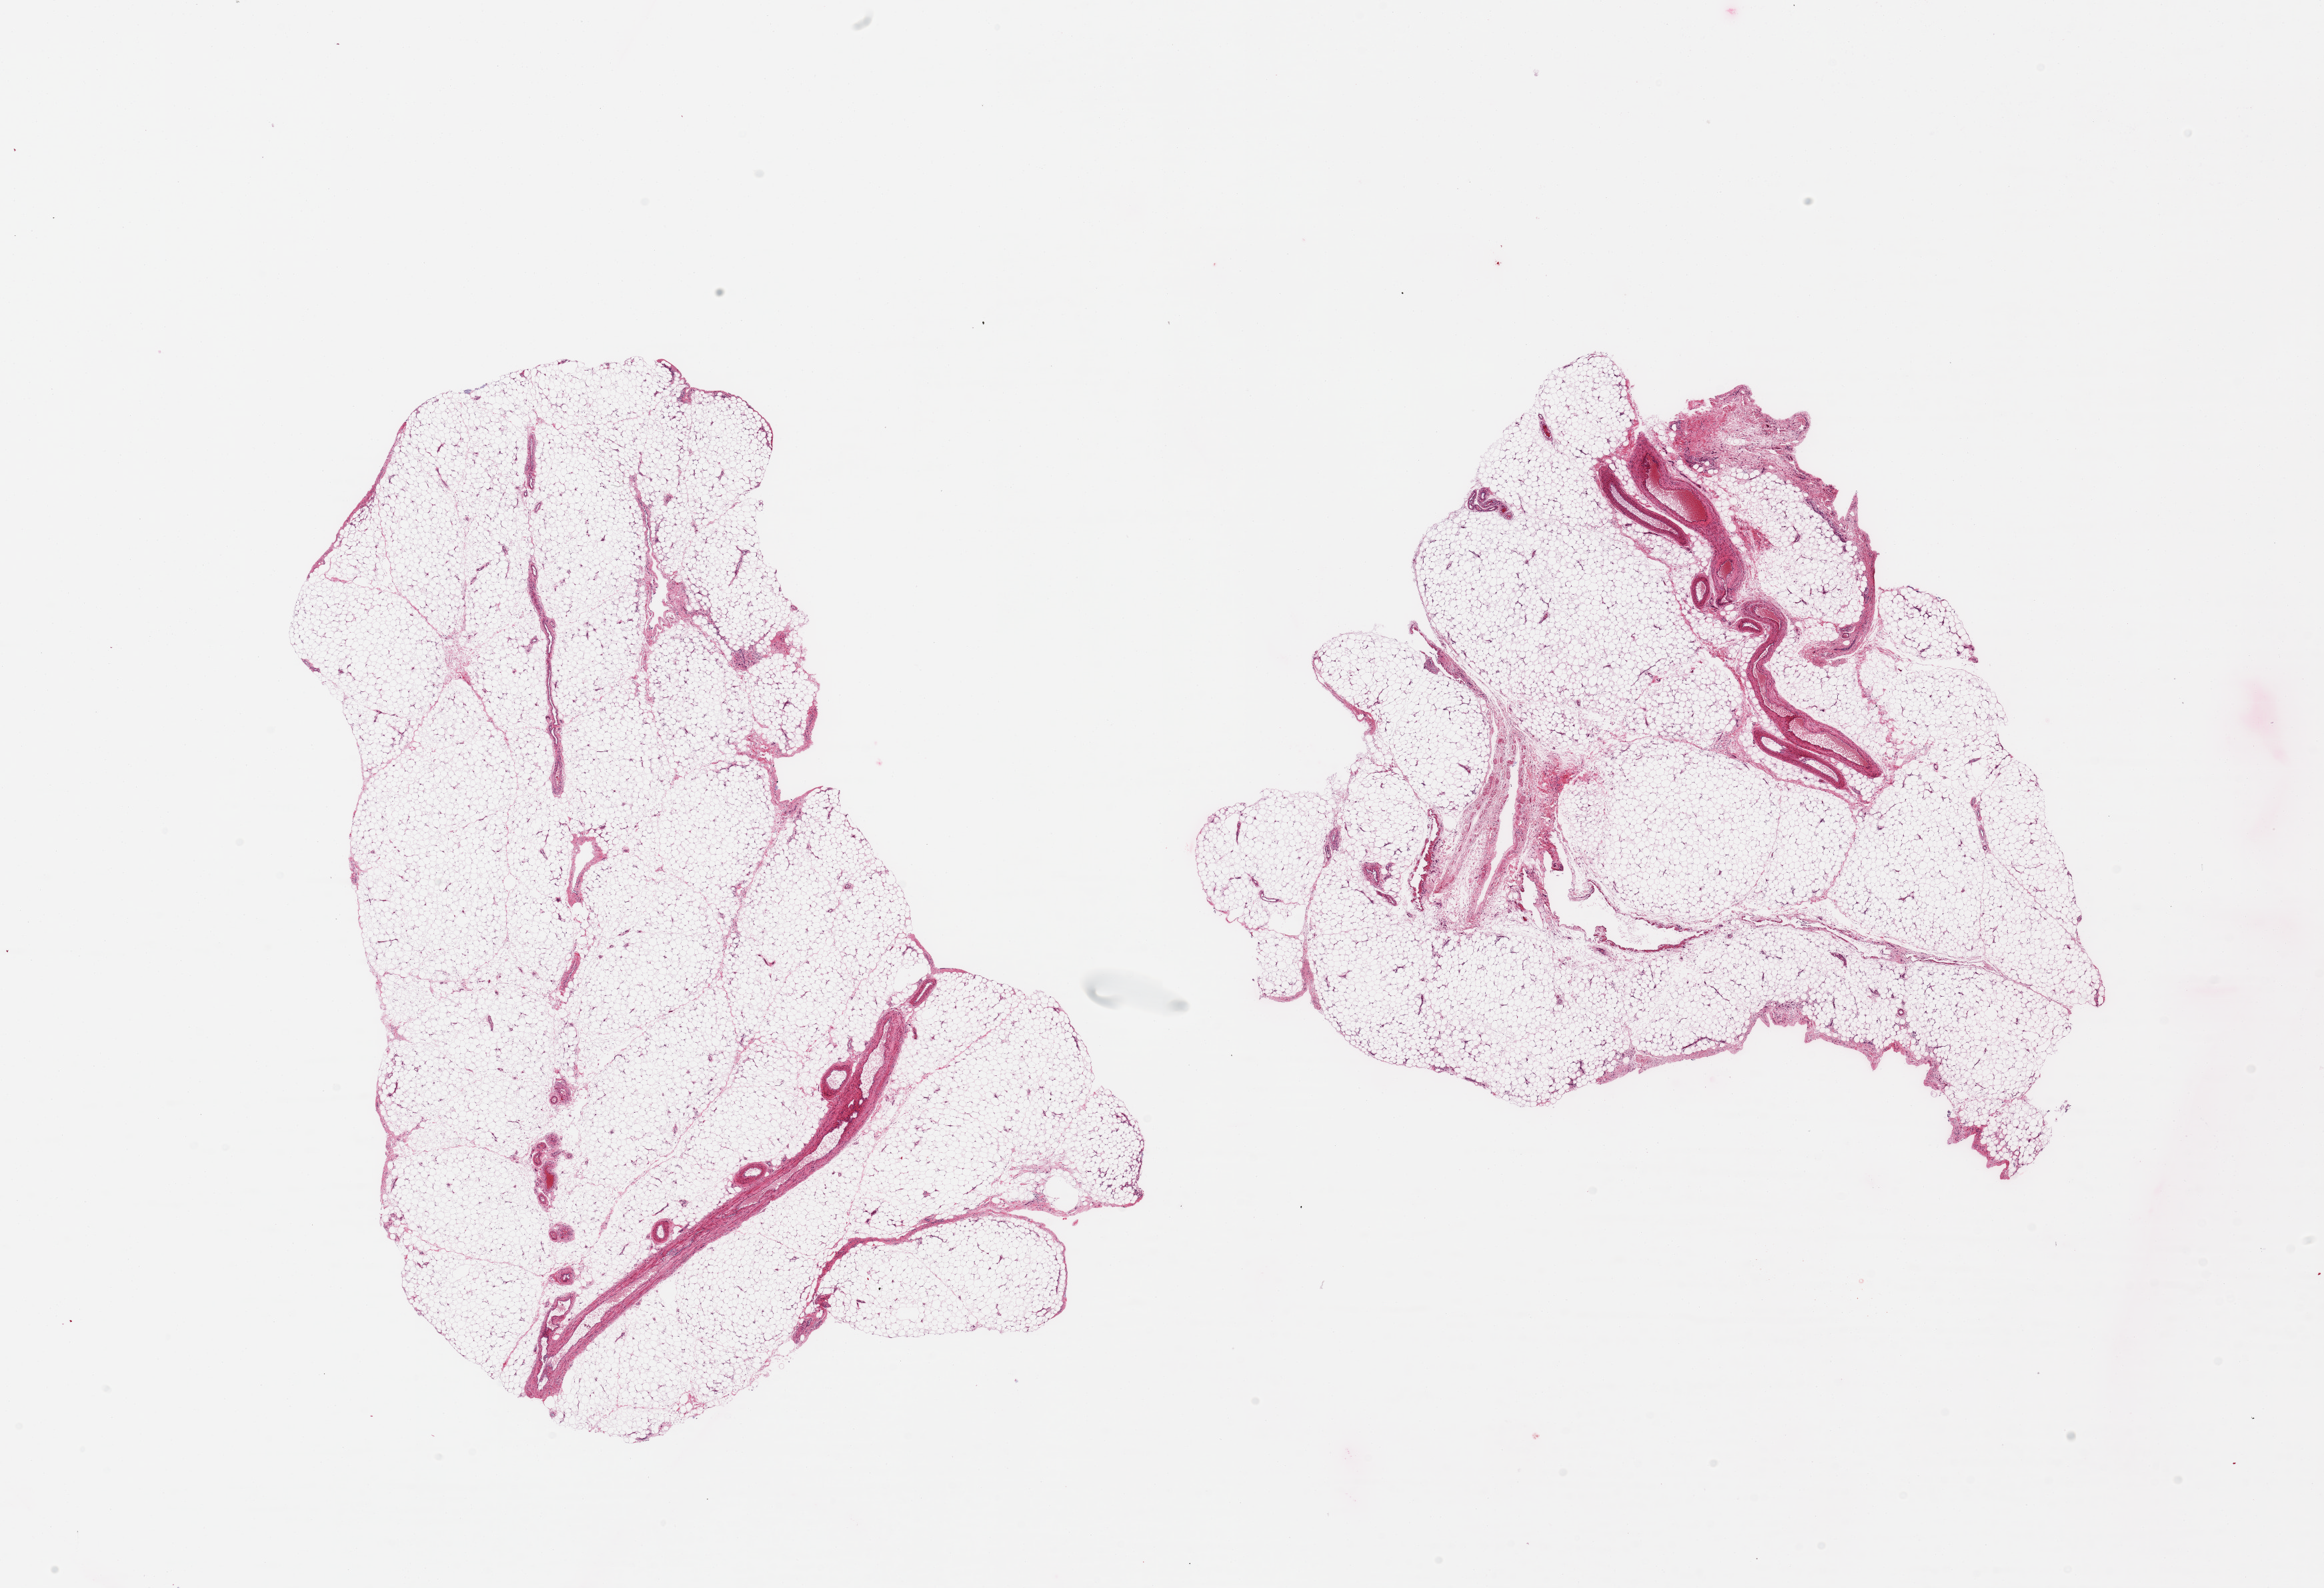
Whole-slide image, haematoxylin and eosin stain — shown as a low-resolution overview of the whole scanned area (about 27.6 x 18.8 mm), PAXgene-fixed paraffin-embedded (PFPE) section, section of omentum (target tissue), tissue donor sample. Female donor.
Review note (as recorded): 2 pieces; 5% fibrovascular content.